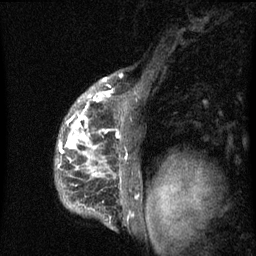
Breast MRI (dynamic contrast-enhanced), one sagittal slice; position 49 of 60 along the scan axis; dynamic contrast-enhanced series, image 2 of 3 at this slice position (ordered by acquisition); 1.5 T; TE 4.2 ms, TR 8 ms; 2 mm slice thickness; 256 × 256 image matrix. Patient: female, 50 years.
Structures marked on this image (semi-automatic segmentation, software-assisted and operator-edited):
- analysis volume of interest (the breast-tissue region the enhancement analysis was run in; not a lesion): box from (x=55, y=90) to (x=142, y=216) px
- tumour enhancement mask (voxels above the 70 % enhancement threshold inside the analysis volume of interest): (x=57, y=91)–(x=121, y=180)